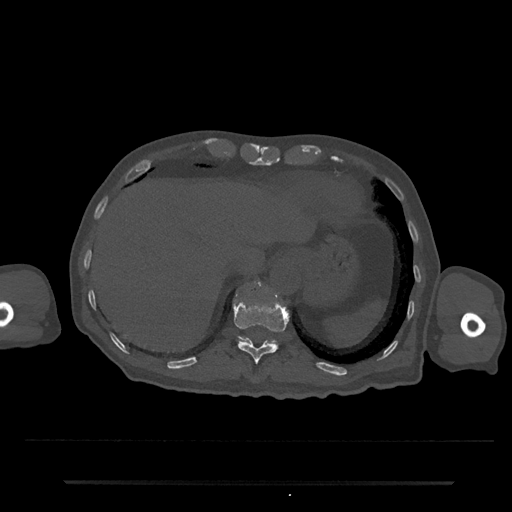
CT including the spine, one axial slice; slice 246 of 797 in the series (ordered by position); reconstruction kernel Br40s/3; bone window (W 1800 / L 400 HU); 0.5 mm slice thickness; 512 × 512 image matrix, field of view 427 × 427 mm. Patient: male, 74 years. Case-level facts recorded for this patient, not image findings: primary cancer: prostate.
Annotated regions visible in this slice (semi-automatically segmented with operator editing):
- T11 vertebra: bounding box <233,296,289,364> (left, top, right, bottom; pixels)
- T12 vertebra: <239,285,275,343>